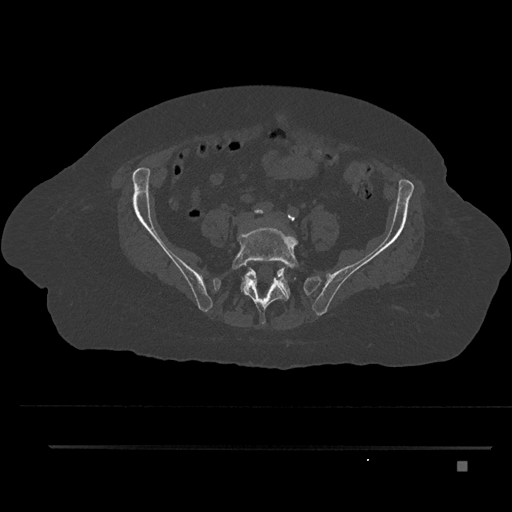
CT including the spine, one axial slice. Slice 37 of 797 in the series (ordered by position). Bone window (W 1800 / L 400 HU). 0.5 mm slice thickness. 512 × 512 image matrix, field of view 437 × 437 mm. Female patient, age 76 years. Case-level facts recorded for this patient, not image findings: primary cancer: lung; vertebrae with lytic lesions (as recorded): T11, L3.
Structures marked on this image (semi-automatic segmentation, software-assisted and operator-edited):
- L5 vertebra: bounding box (x1, y1, x2, y2) in pixels: (232, 227, 299, 324)